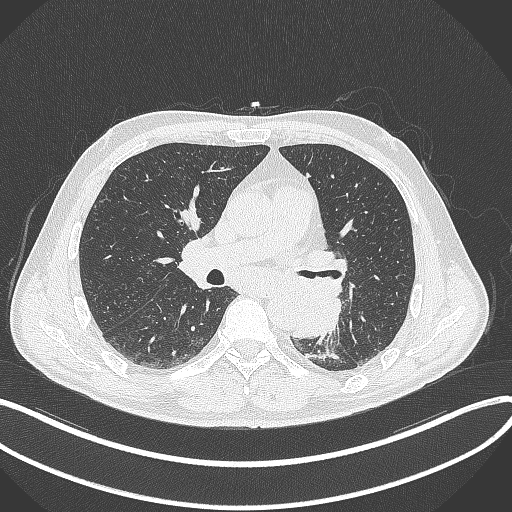
Chest CT, one axial slice; slice 186 of 329 in the series (ordered by position); reconstruction kernel B70f; lung window (W 1500 / L -600 HU); 1 mm slice thickness; 512 × 512 image matrix. Patient: male, 59 years. From the clinical record (not read from this slice): clinical TNM (as recorded): T2a N2 M0.
Outlined on this slice (bounding box drawn by a radiologist):
- lung tumour (recorded histology: squamous cell carcinoma): bounding box (x1, y1, x2, y2) in pixels: (290, 275, 347, 340)